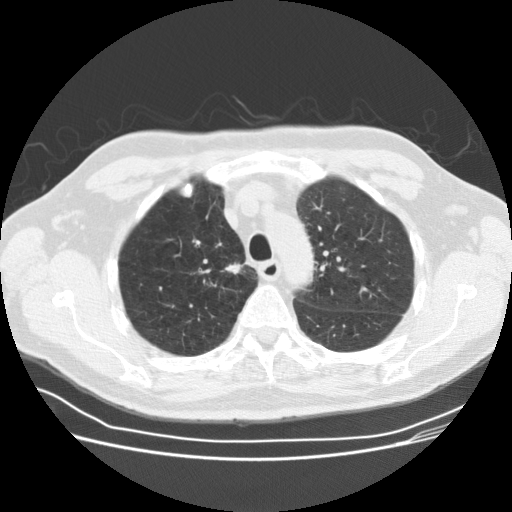
Axial slice from a low-dose chest CT screening exam; third annual screen; lung window (W 1500 / L -600 HU); 2.5 mm slice thickness; slice 123 of 164 in the series. Male, age 69 years at enrolment.
- Expert reader's lesion annotation, bounding box [x1, y1, x2, y2] px = [221, 256, 259, 289].
- Screening reader's record for this exam (one nodule recorded; not confirmed to be the boxed lesion): non-calcified nodule or mass ≥4 mm, right upper lobe, 12 × 10 mm, spiculated (stellate) margins, soft tissue attenuation, pre-existing on the prior screen: yes; interval growth: yes.
- Official screen result: positive, other.
- Participant outcome: lung cancer diagnosed 36 days after this screen — squamous cell carcinoma, NOS, right upper lobe, moderately differentiated (G2), stage IA (AJCC 6th edition), 9 mm at pathology.